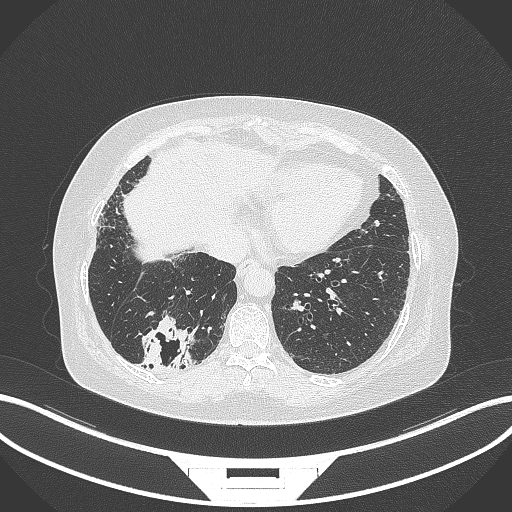
Chest CT, one axial slice; position 54 of 296 along the scan axis; 120 kVp; lung window (W 1500 / L -600 HU); 1 mm slice thickness; 512 × 512 image matrix, field of view 400 × 400 mm. Female patient, age 65 years. From the clinical record (not read from this slice): clinical TNM (as recorded): T2b N1 M0.
Annotated regions visible in this slice (rectangle marked by the reading radiologist):
- lung tumour (recorded histology: adenocarcinoma): bounding box [x1, y1, x2, y2] px = [132, 311, 198, 371]